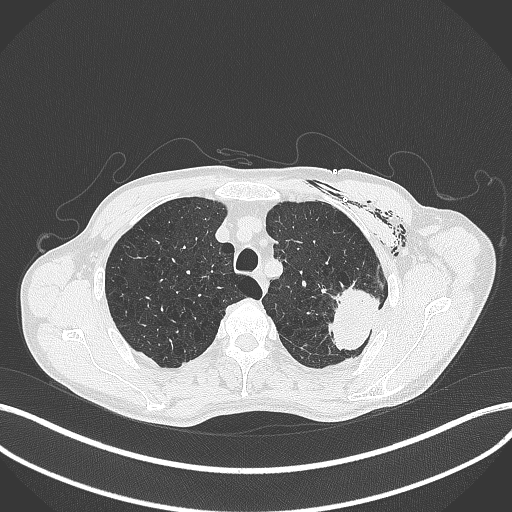
Chest CT, one axial slice. Slice 331 of 457 in the series (ordered by position). Reconstruction kernel B70f. Lung window (W 1500 / L -600 HU). 1 mm slice thickness. 512 × 512 image matrix, field of view 400 × 400 mm. Patient: male, 58 years. Case-level facts recorded for this patient, not image findings: clinical TNM (as recorded): T3 N0 M0.
Outlined on this slice (rectangle marked by the reading radiologist):
- lung tumour (recorded histology: adenocarcinoma): bounding box [x1, y1, x2, y2] px = [327, 283, 382, 353]